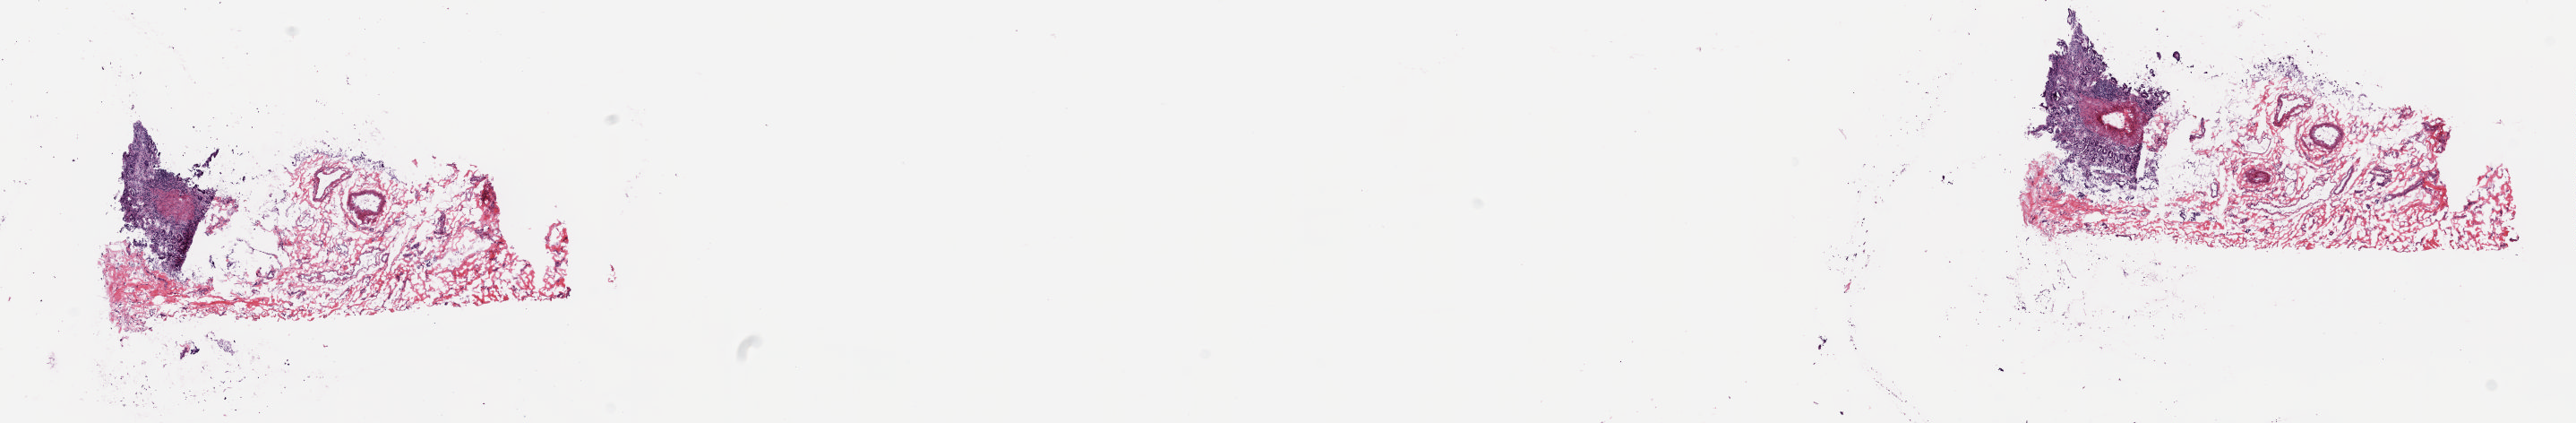
Digitized H&E tissue section (whole slide), a low-resolution overview of the entire scanned area, about 22.8 x 3.7 mm (from a 20x scan), frozen section, solid tissue normal (non-tumour tissue) sample from the pancreas. Male, age 64 years at initial diagnosis. Slide review estimates, as recorded: tumour cells 0%, tumour nuclei 0%, normal cells 15%, stromal cells 85%, necrosis 0%. Inflammatory infiltration, as recorded: lymphocyte infiltration 30%, monocyte infiltration 2%, neutrophil infiltration 2%.
- this section: solid tissue normal (non-tumour) sample from the same patient
- patient diagnosis: Infiltrating duct carcinoma, NOS (head of pancreas)